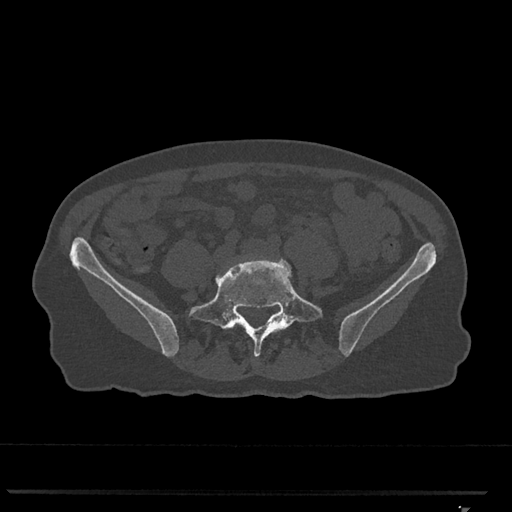
CT including the spine, one axial slice. Position 159 of 793 along the scan axis. Reconstruction kernel Br40s/3. 120 kVp. Bone window (W 1800 / L 400 HU). 0.5 mm slice thickness. 512 × 512 image matrix, field of view 380 × 380 mm. Patient: female, 62 years. From the clinical record (not read from this slice): primary cancer: renal.
Structures marked on this image (semi-automatically segmented with operator editing):
- L4 vertebra: bounding box [x1, y1, x2, y2] px = [215, 258, 258, 279]
- L5 vertebra: [189, 259, 323, 357]